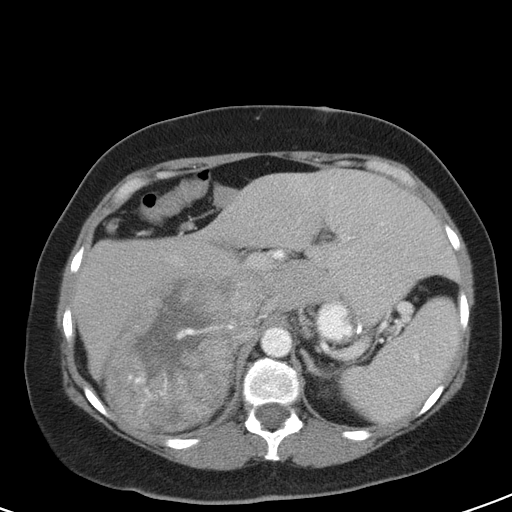
Contrast-enhanced abdominal CT, one axial slice. Position 75 of 126 along the scan axis. Intravenous contrast given. Soft-tissue window (W 400 / L 40 HU). 5 mm slice thickness. 512 × 512 image matrix. Patient: female, 51 years. Case-level facts recorded for this patient, not image findings: diagnosis: adrenocortical carcinoma; tumour side: right adrenal; tumour size at pathology: 17 cm; Ki-67 index: 12 %; stage (as recorded): 2.
Annotated regions visible in this slice (semi-automatic segmentation, software-assisted and operator-edited):
- mass: bounding box <106,270,259,432> (left, top, right, bottom; pixels)